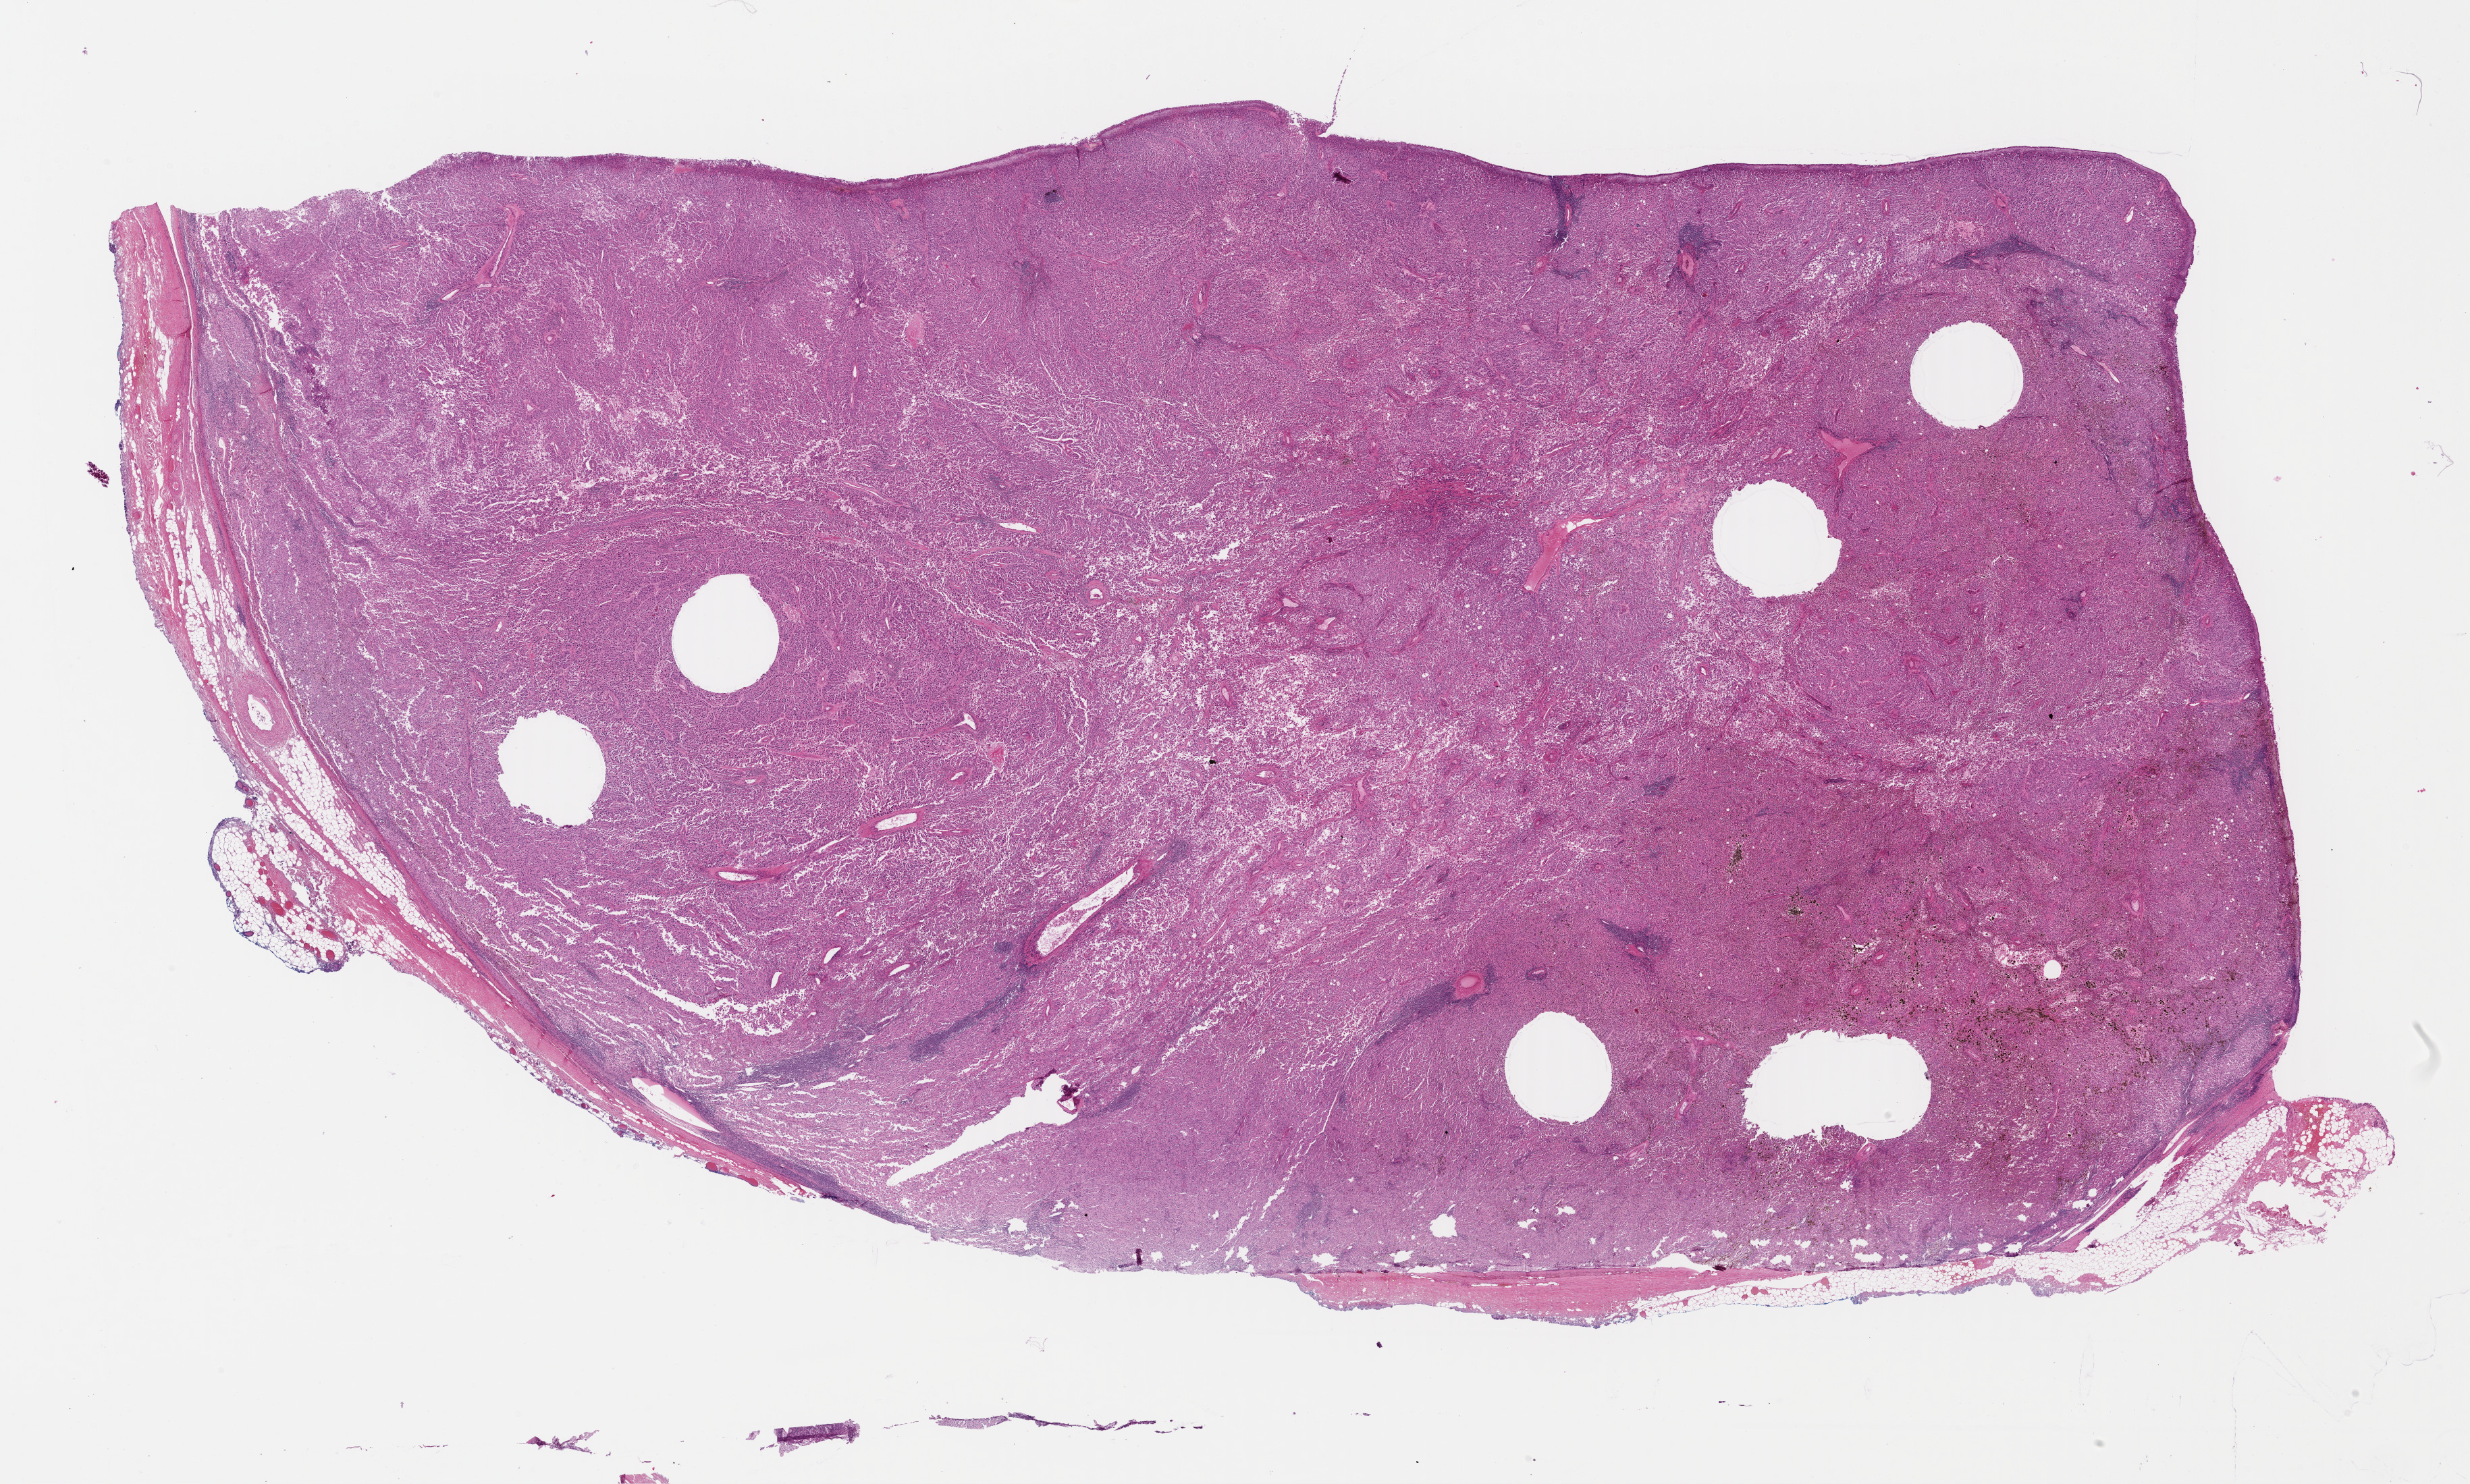
H&E whole-slide image — low-resolution overview of the scanned area, about 28.8 x 17.3 mm (from a 40x scan), FFPE section, sample: primary tumour, skin. Male, age 51 years at initial diagnosis.
Pathologic diagnosis: Malignant melanoma, NOS.